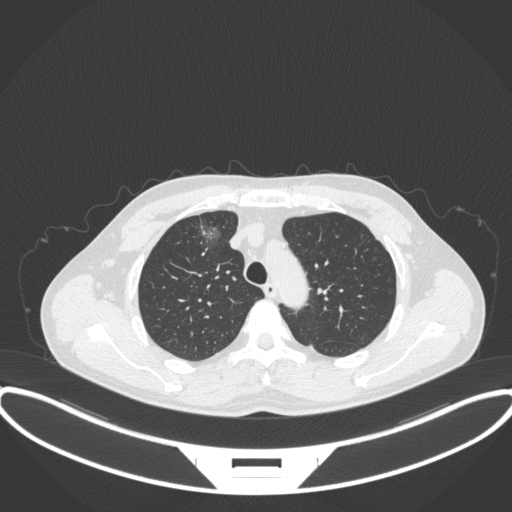
Chest CT, one axial slice; slice 280 of 395 in the series (ordered by position); 120 kVp; lung window (W 1500 / L -600 HU); 512 × 512 image matrix. Patient: male, 60 years. From the clinical record (not read from this slice): clinical TNM (as recorded): T1c N0 M0.
Outlined on this slice (bounding box drawn by a radiologist):
- lung tumour (recorded histology: adenocarcinoma): box from (x=190, y=217) to (x=225, y=256) px